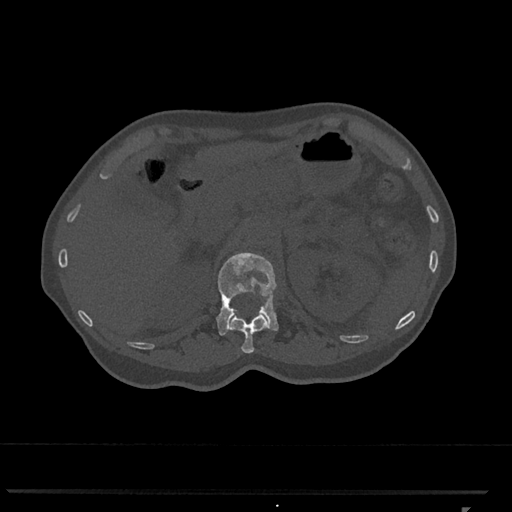
CT including the spine, one axial slice. Slice 428 of 793 in the series (ordered by position). Reconstruction kernel Br40s/3. 120 kVp. Bone window (W 1800 / L 400 HU). 0.5 mm slice thickness. 512 × 512 image matrix, field of view 380 × 380 mm. Female patient, age 62 years. Case-level facts recorded for this patient, not image findings: primary cancer: renal.
Outlined on this slice (semi-automatic segmentation, software-assisted and operator-edited):
- L1 vertebra: bounding box (x1, y1, x2, y2) in pixels: (216, 253, 279, 335)
- T12 vertebra: (229, 312, 268, 354)